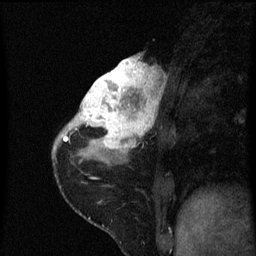
Breast MRI (dynamic contrast-enhanced), one sagittal slice. Slice 24 of 60 in the series (ordered by position). Dynamic contrast-enhanced series, image 2 of 3 at this slice position (ordered by acquisition). 1.5 T. TE 4.2 ms, TR 8 ms. 2 mm slice thickness. 256 × 256 image matrix, field of view 180 × 180 mm. Patient: female, 38 years.
Annotated regions visible in this slice (semi-automatic segmentation, software-assisted and operator-edited):
- analysis volume of interest (the breast-tissue region the enhancement analysis was run in; not a lesion): bounding box <80,54,165,151> (left, top, right, bottom; pixels)
- tumour enhancement mask (voxels above the 70 % enhancement threshold inside the analysis volume of interest): <80,56,161,151>